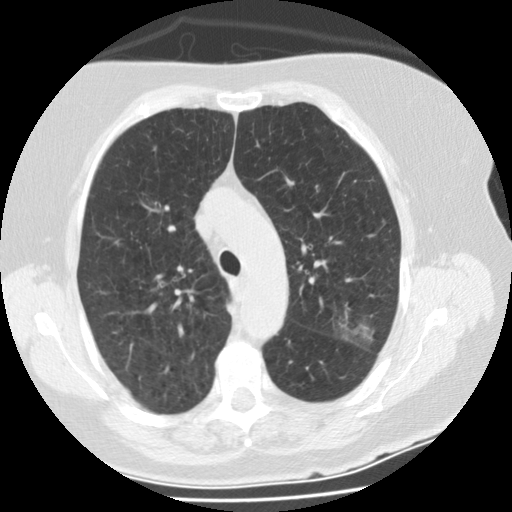
Axial slice from a low-dose chest CT screening exam; second screening round (one year after baseline); lung window (W 1500 / L -600 HU); 120 kVp; slice 79 of 297 in the series; 512 × 512 image matrix, field of view 321 × 321 mm. Female, age 74 years at enrolment. Former smoker at enrolment.
Expert-annotated lung lesion, bounding box (x1, y1, x2, y2) in pixels: (327, 307, 387, 360). The screening reader recorded 3 non-calcified nodules or masses ≥4 mm on this exam; which of them this box marks is not recorded. Participant outcome: lung cancer diagnosed 68 days after this screen — bronchiolo-alveolar adenocarcinoma, NOS, left upper lobe, stage IA (AJCC 6th edition), 20 mm at pathology.